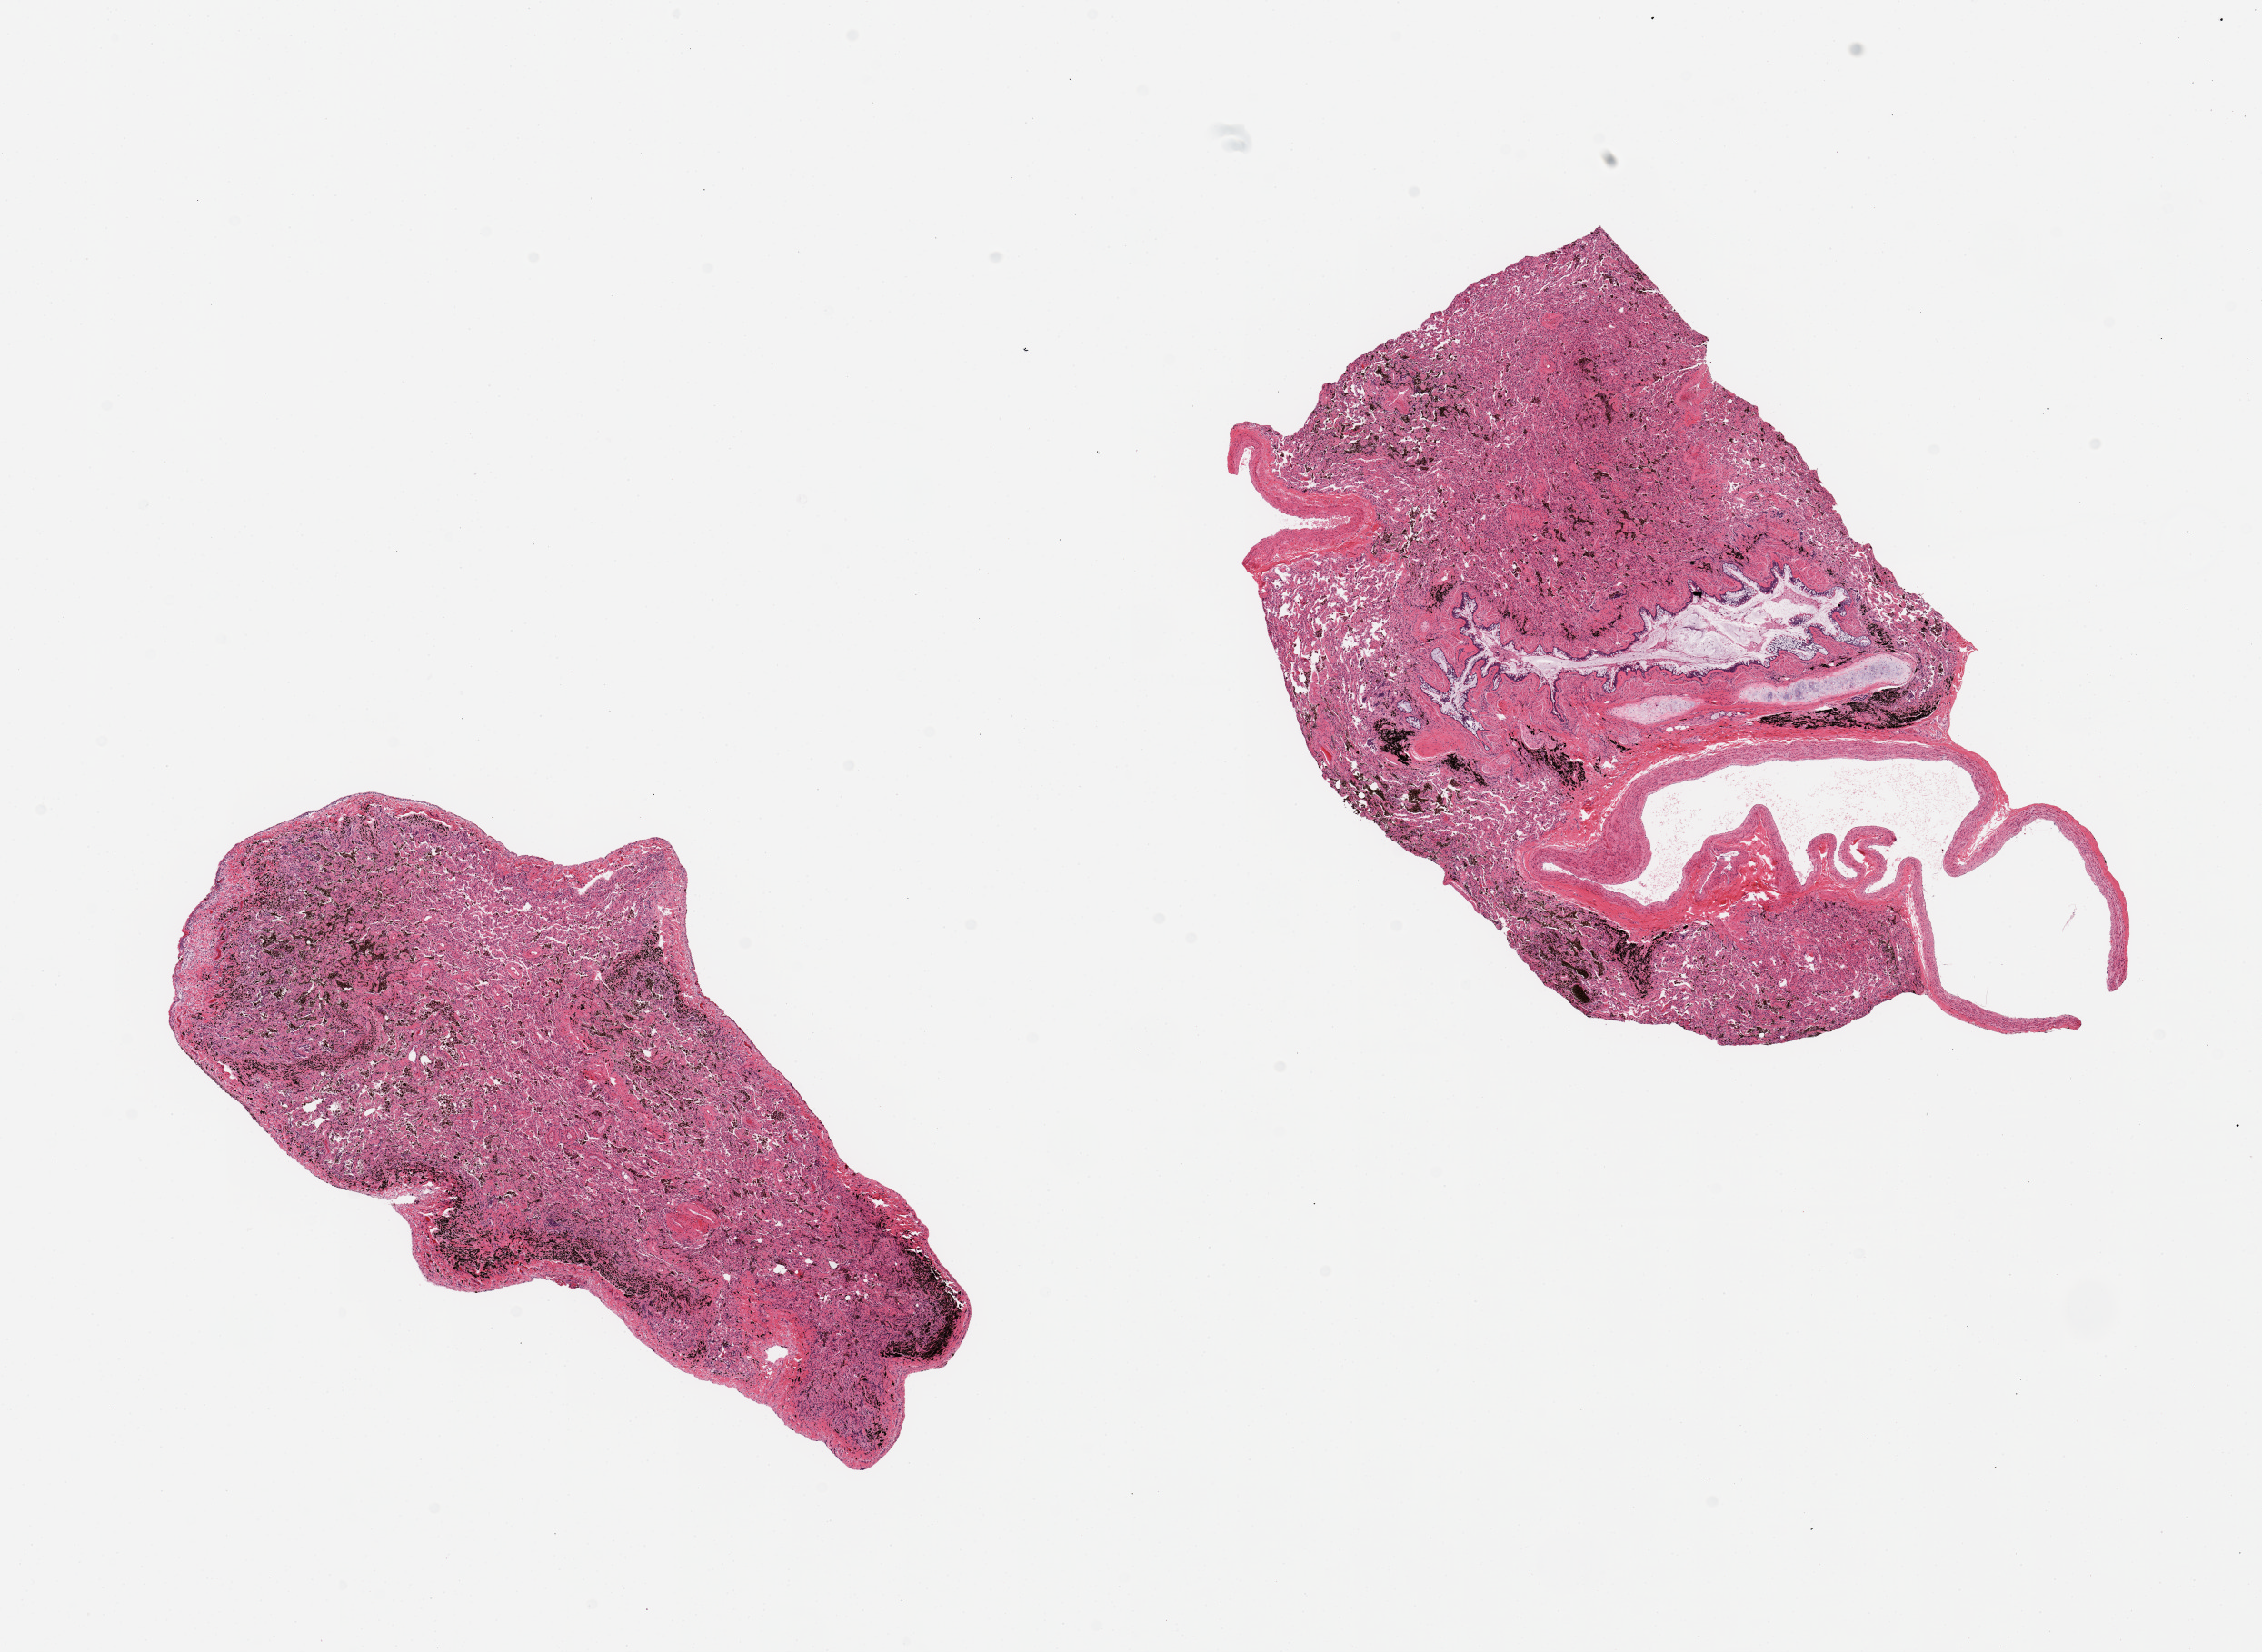
Whole-slide image, haematoxylin and eosin stain, whole scanned area (about 19.7 x 14.4 mm, acquisition: 20x scan) shown as a low-resolution overview, PAXgene-fixed, paraffin-embedded tissue, sampled site (target tissue): lung, tissue donor sample.
- reviewer comment on this tissue sample: 2 pieces; marked fibrosis and pigmented macrophages; 1 piece contains > 50% bronchus and large blood vessels